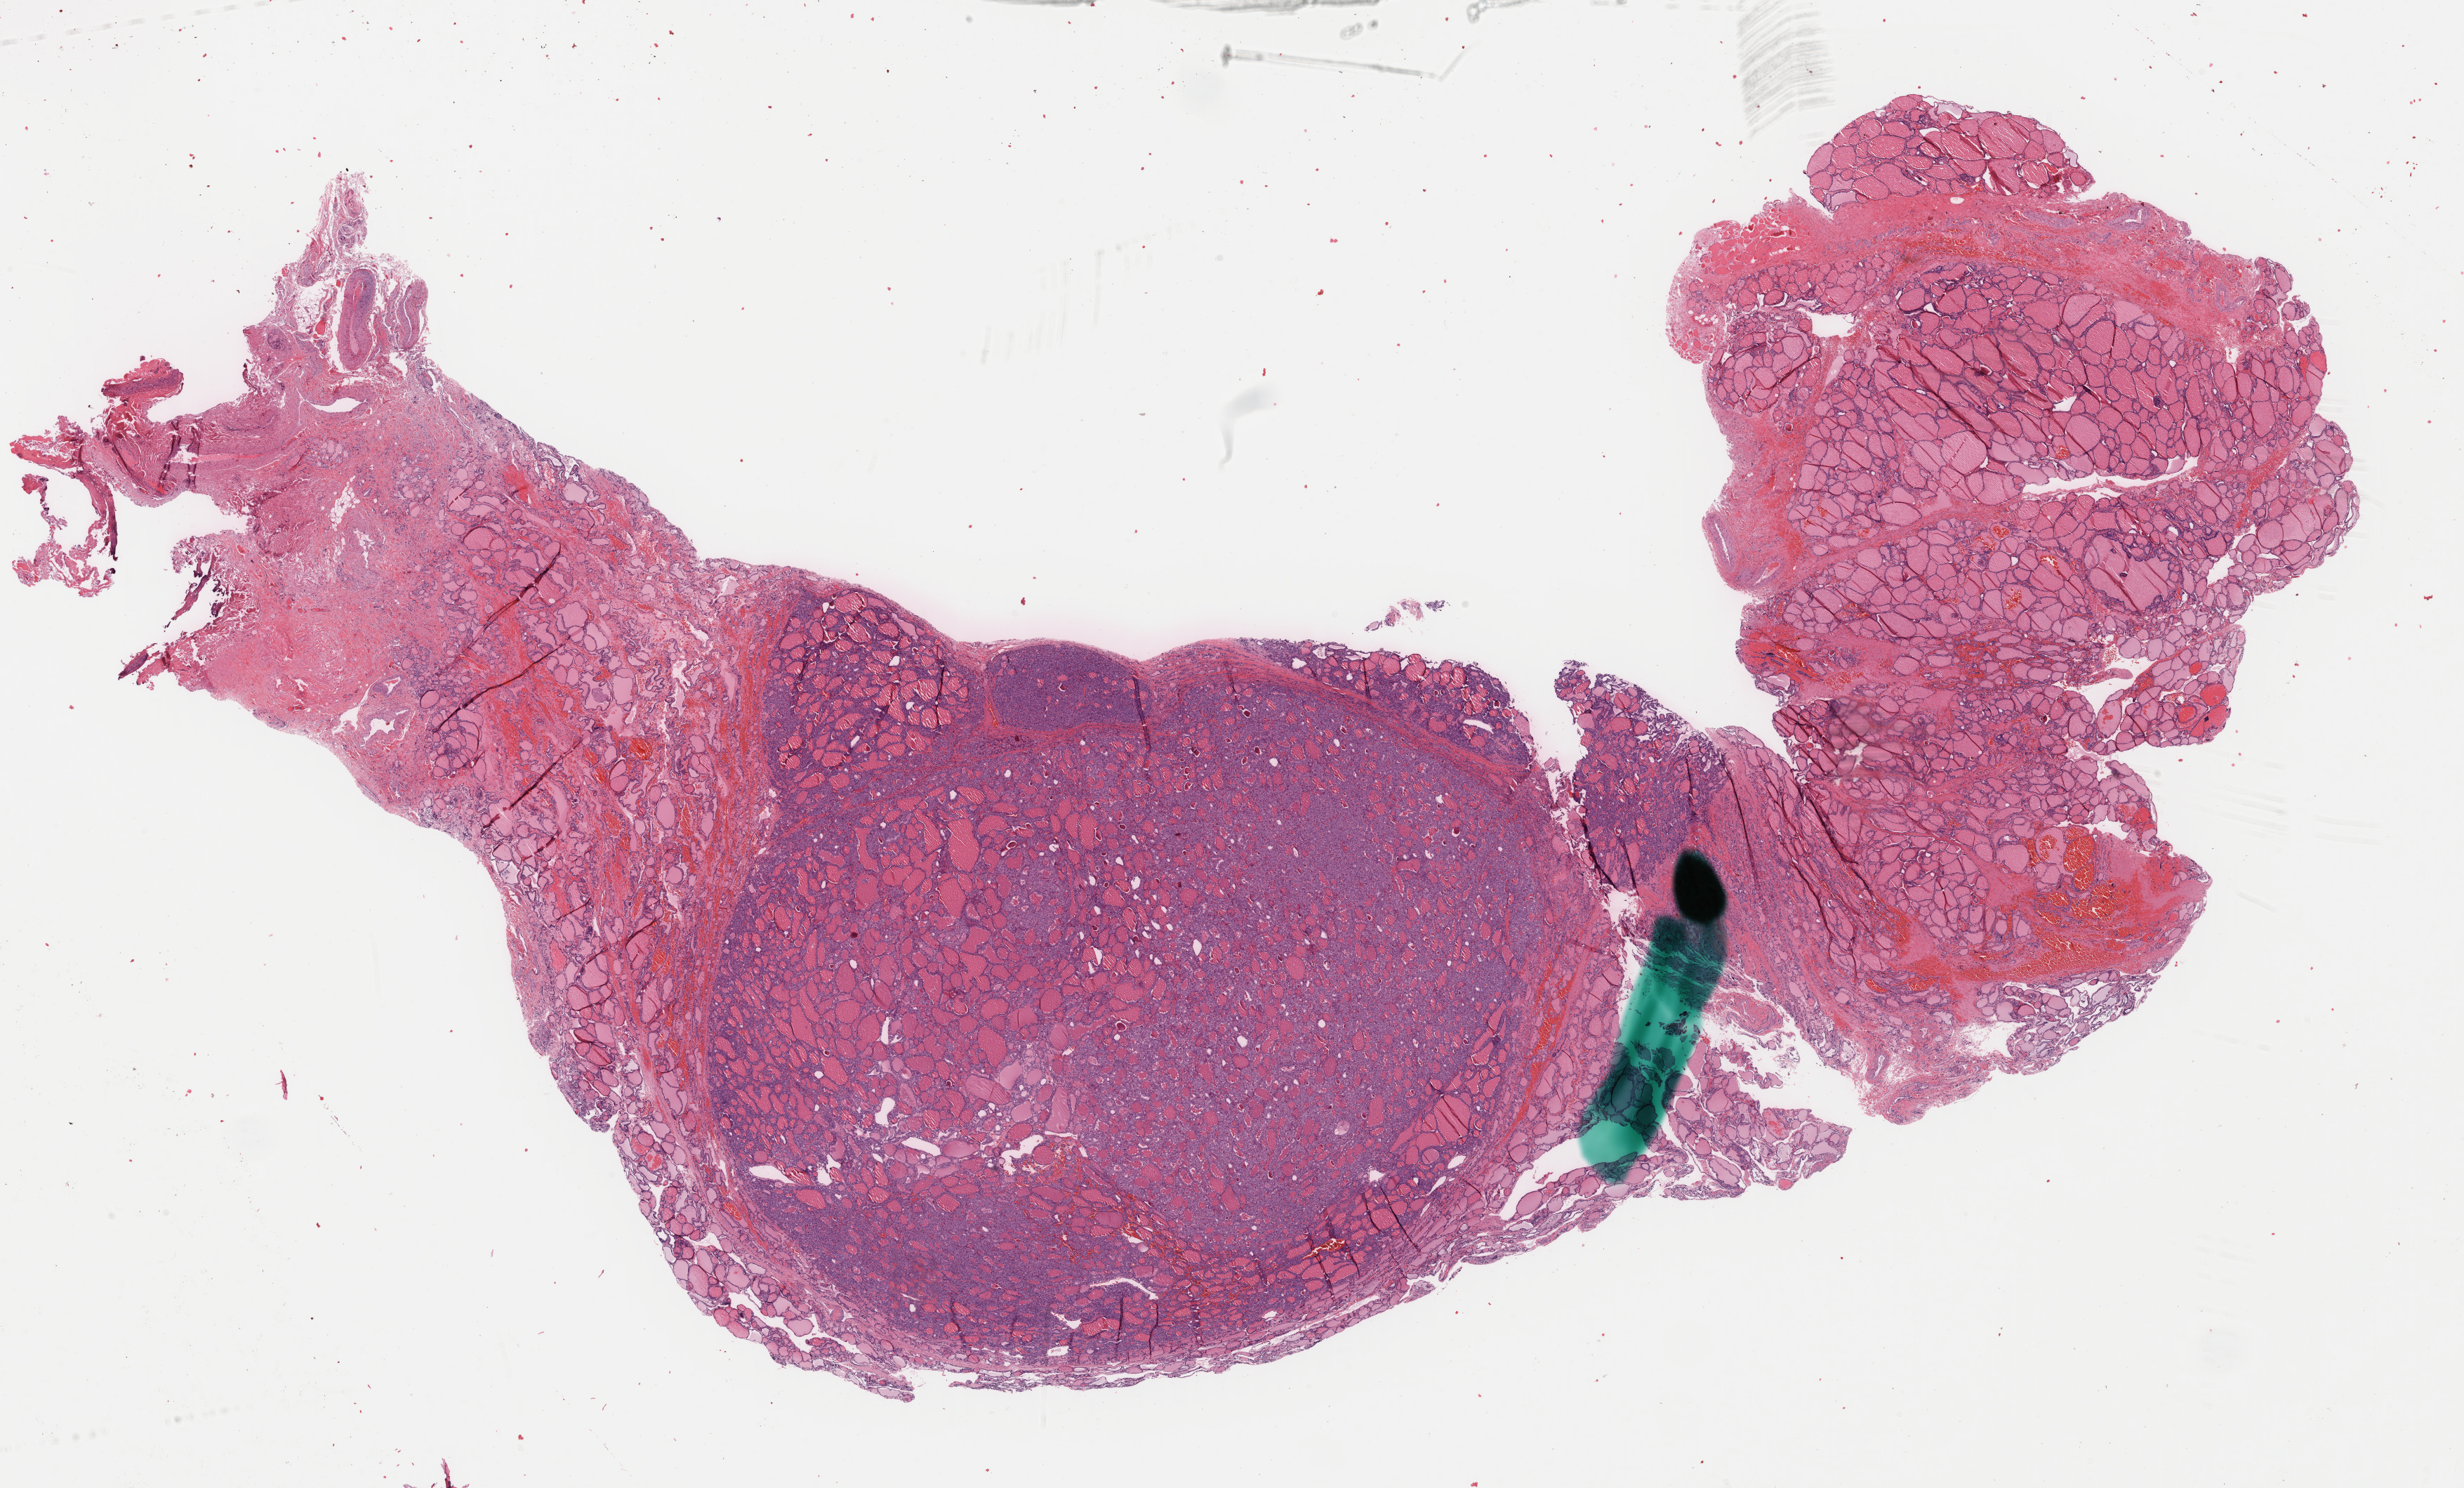
Digitized H&E tissue section (whole slide), shown as a low-resolution overview of the whole scanned area (about 27.7 x 16.7 mm, slide scanned at 40x). Formalin-fixed paraffin-embedded (FFPE) diagnostic section. Primary tumour sample from the thyroid. Female patient; age at initial diagnosis 41 years.
- AJCC pathologic stage: I (6th edition)
- histologic diagnosis: Papillary adenocarcinoma, NOS (thyroid gland)
- lymph nodes positive (case pathology): 0 of 1 examined